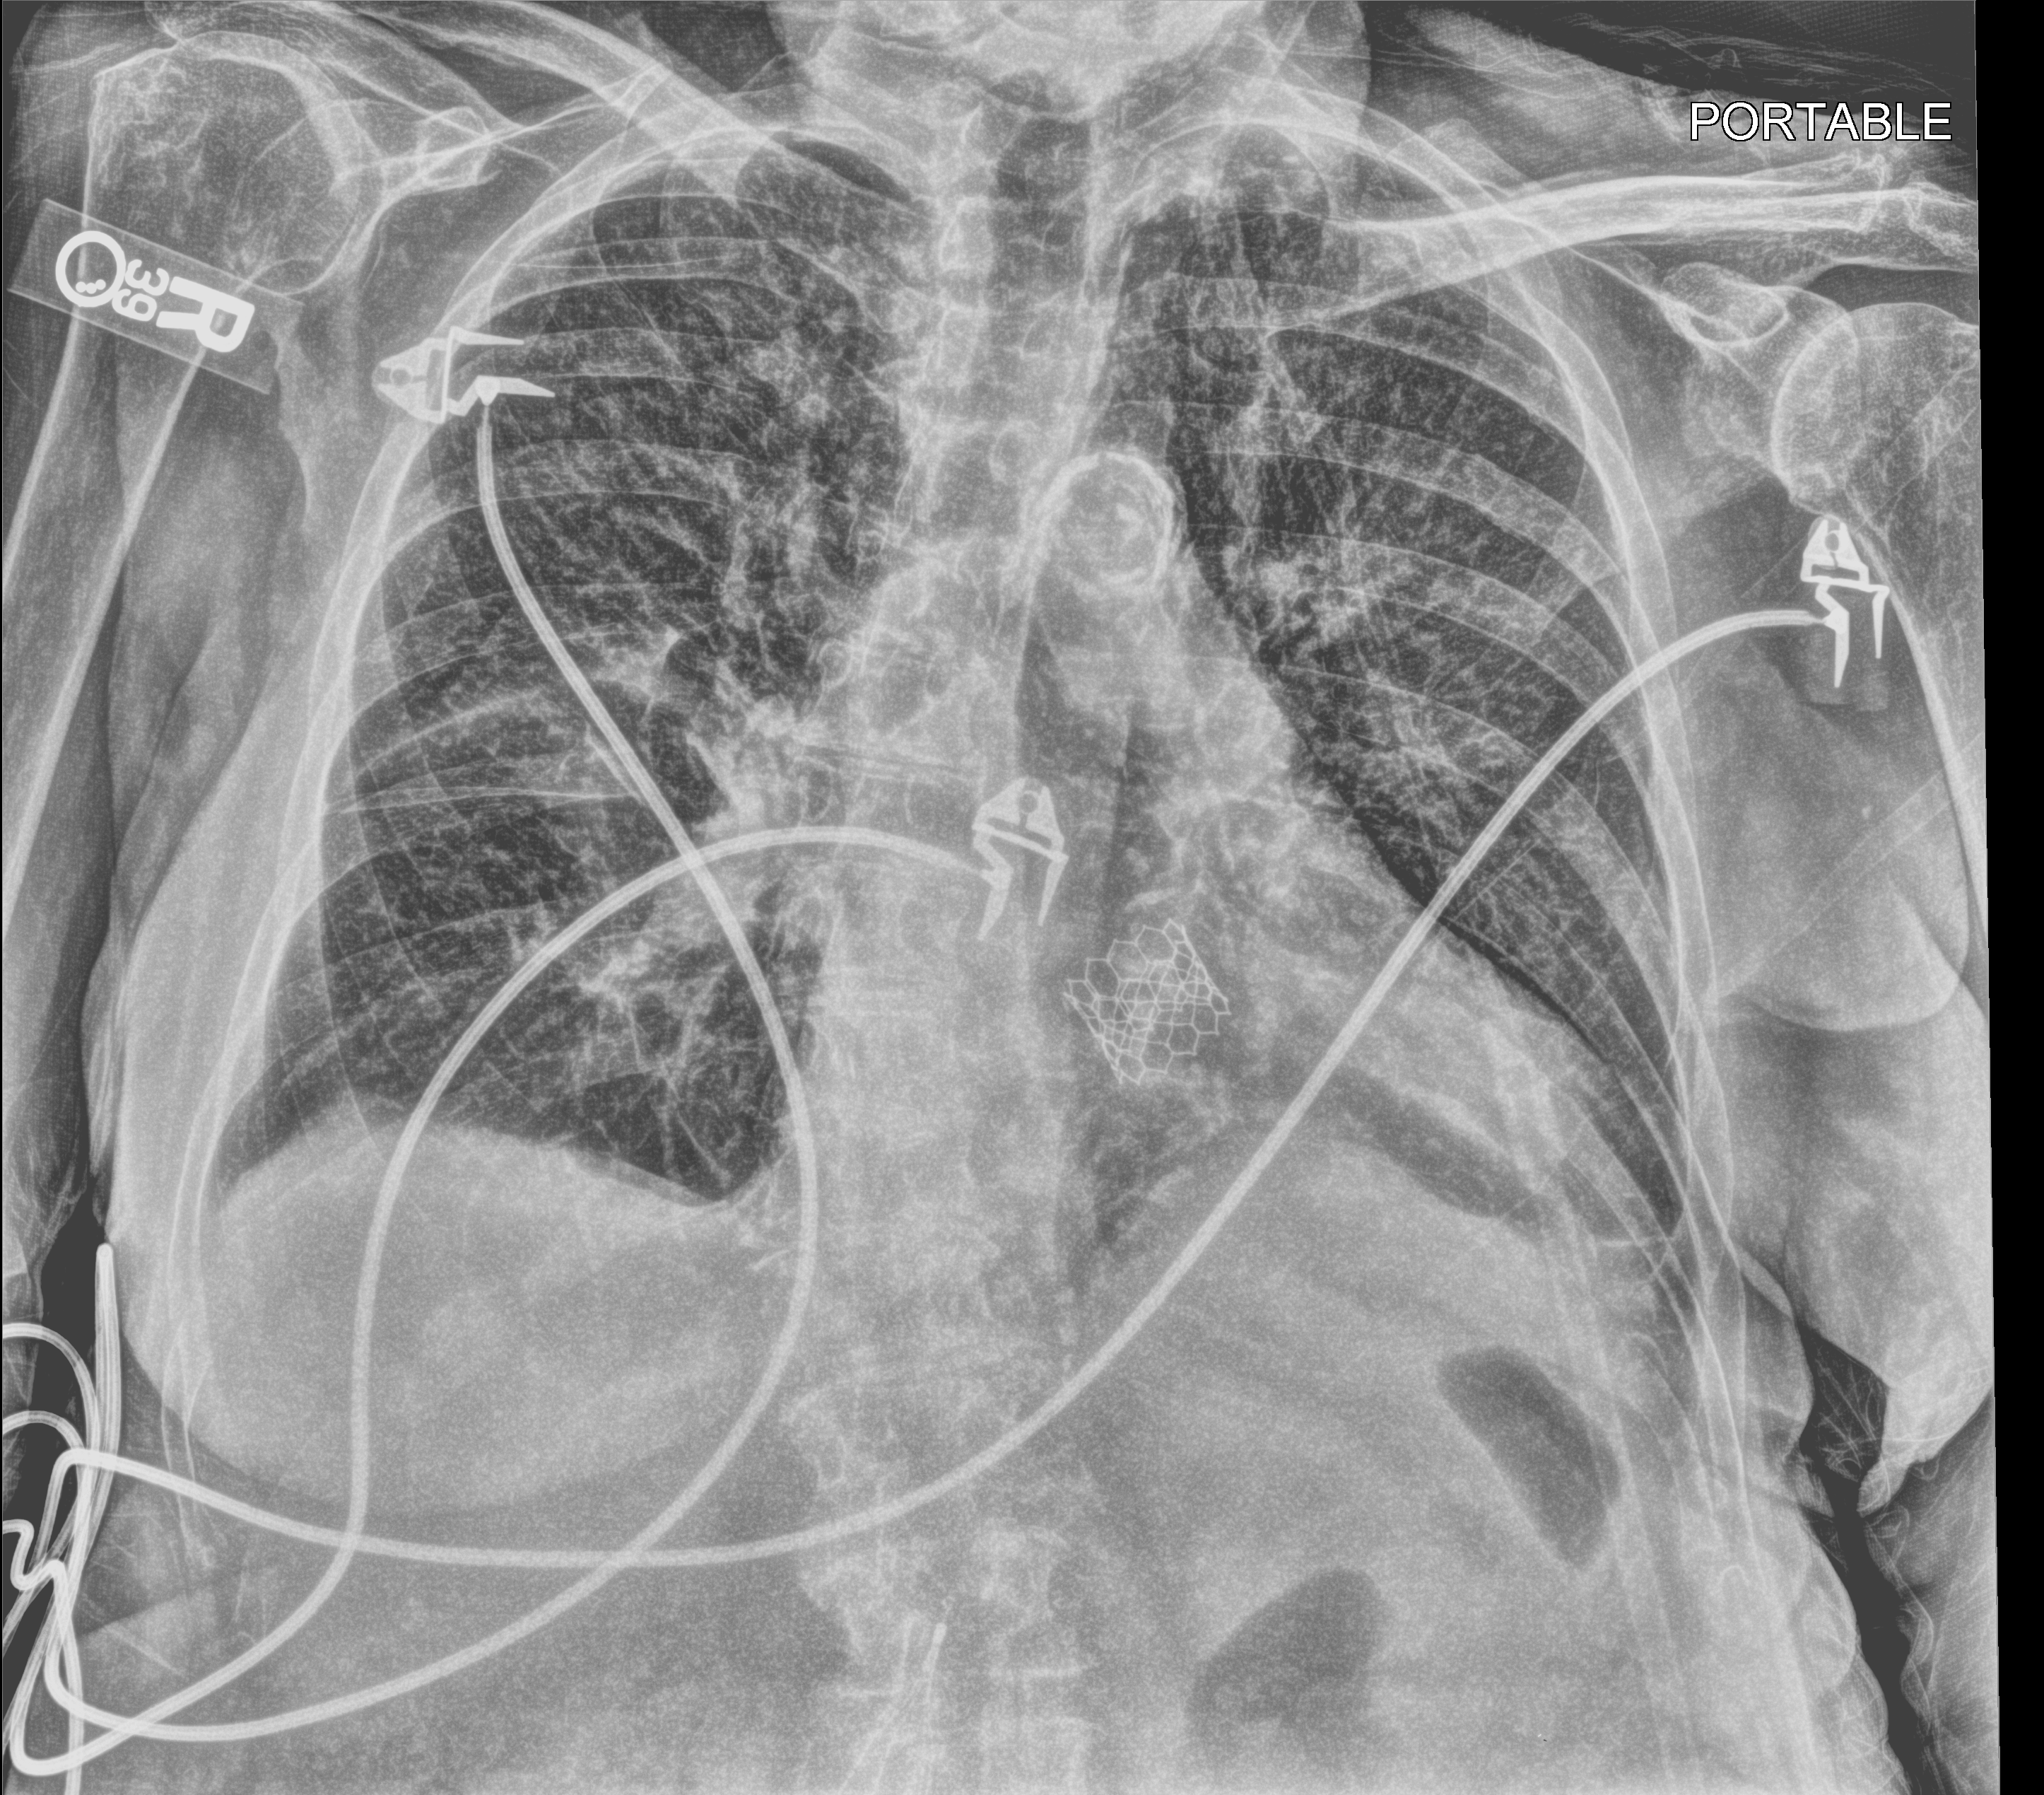
Bedside chest radiograph (computed radiography); anteroposterior (AP) projection. Patient hospitalised with COVID-19; female, aged 75–90 years.
Hospital-stay facts (about this admission, not read from this image; timing relative to this image not recorded):
- admitted to intensive care during this hospital stay: no
- mechanically ventilated during this hospital stay: no